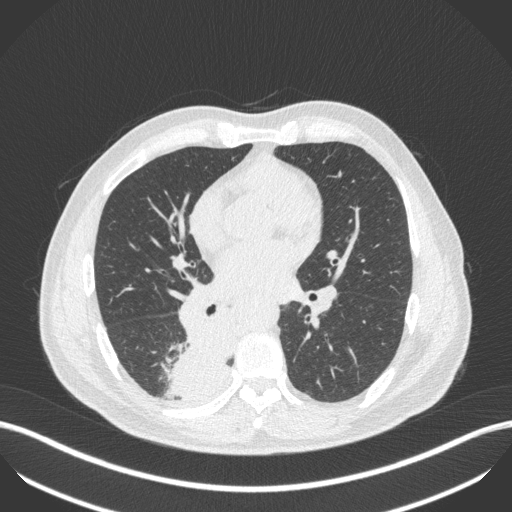
Chest CT, one axial slice; slice 233 of 451 in the series (ordered by position); reconstruction kernel B31f; lung window (W 1500 / L -600 HU); 1 mm slice thickness; 512 × 512 image matrix, field of view 400 × 400 mm. Male patient, age 61 years. From the clinical record (not read from this slice): clinical TNM (as recorded): T1 N0 M0; histopathological grade: G3.
Structures marked on this image (bounding box drawn by a radiologist):
- lung tumour (recorded histology: small cell carcinoma): bounding box <150,313,236,402> (left, top, right, bottom; pixels)